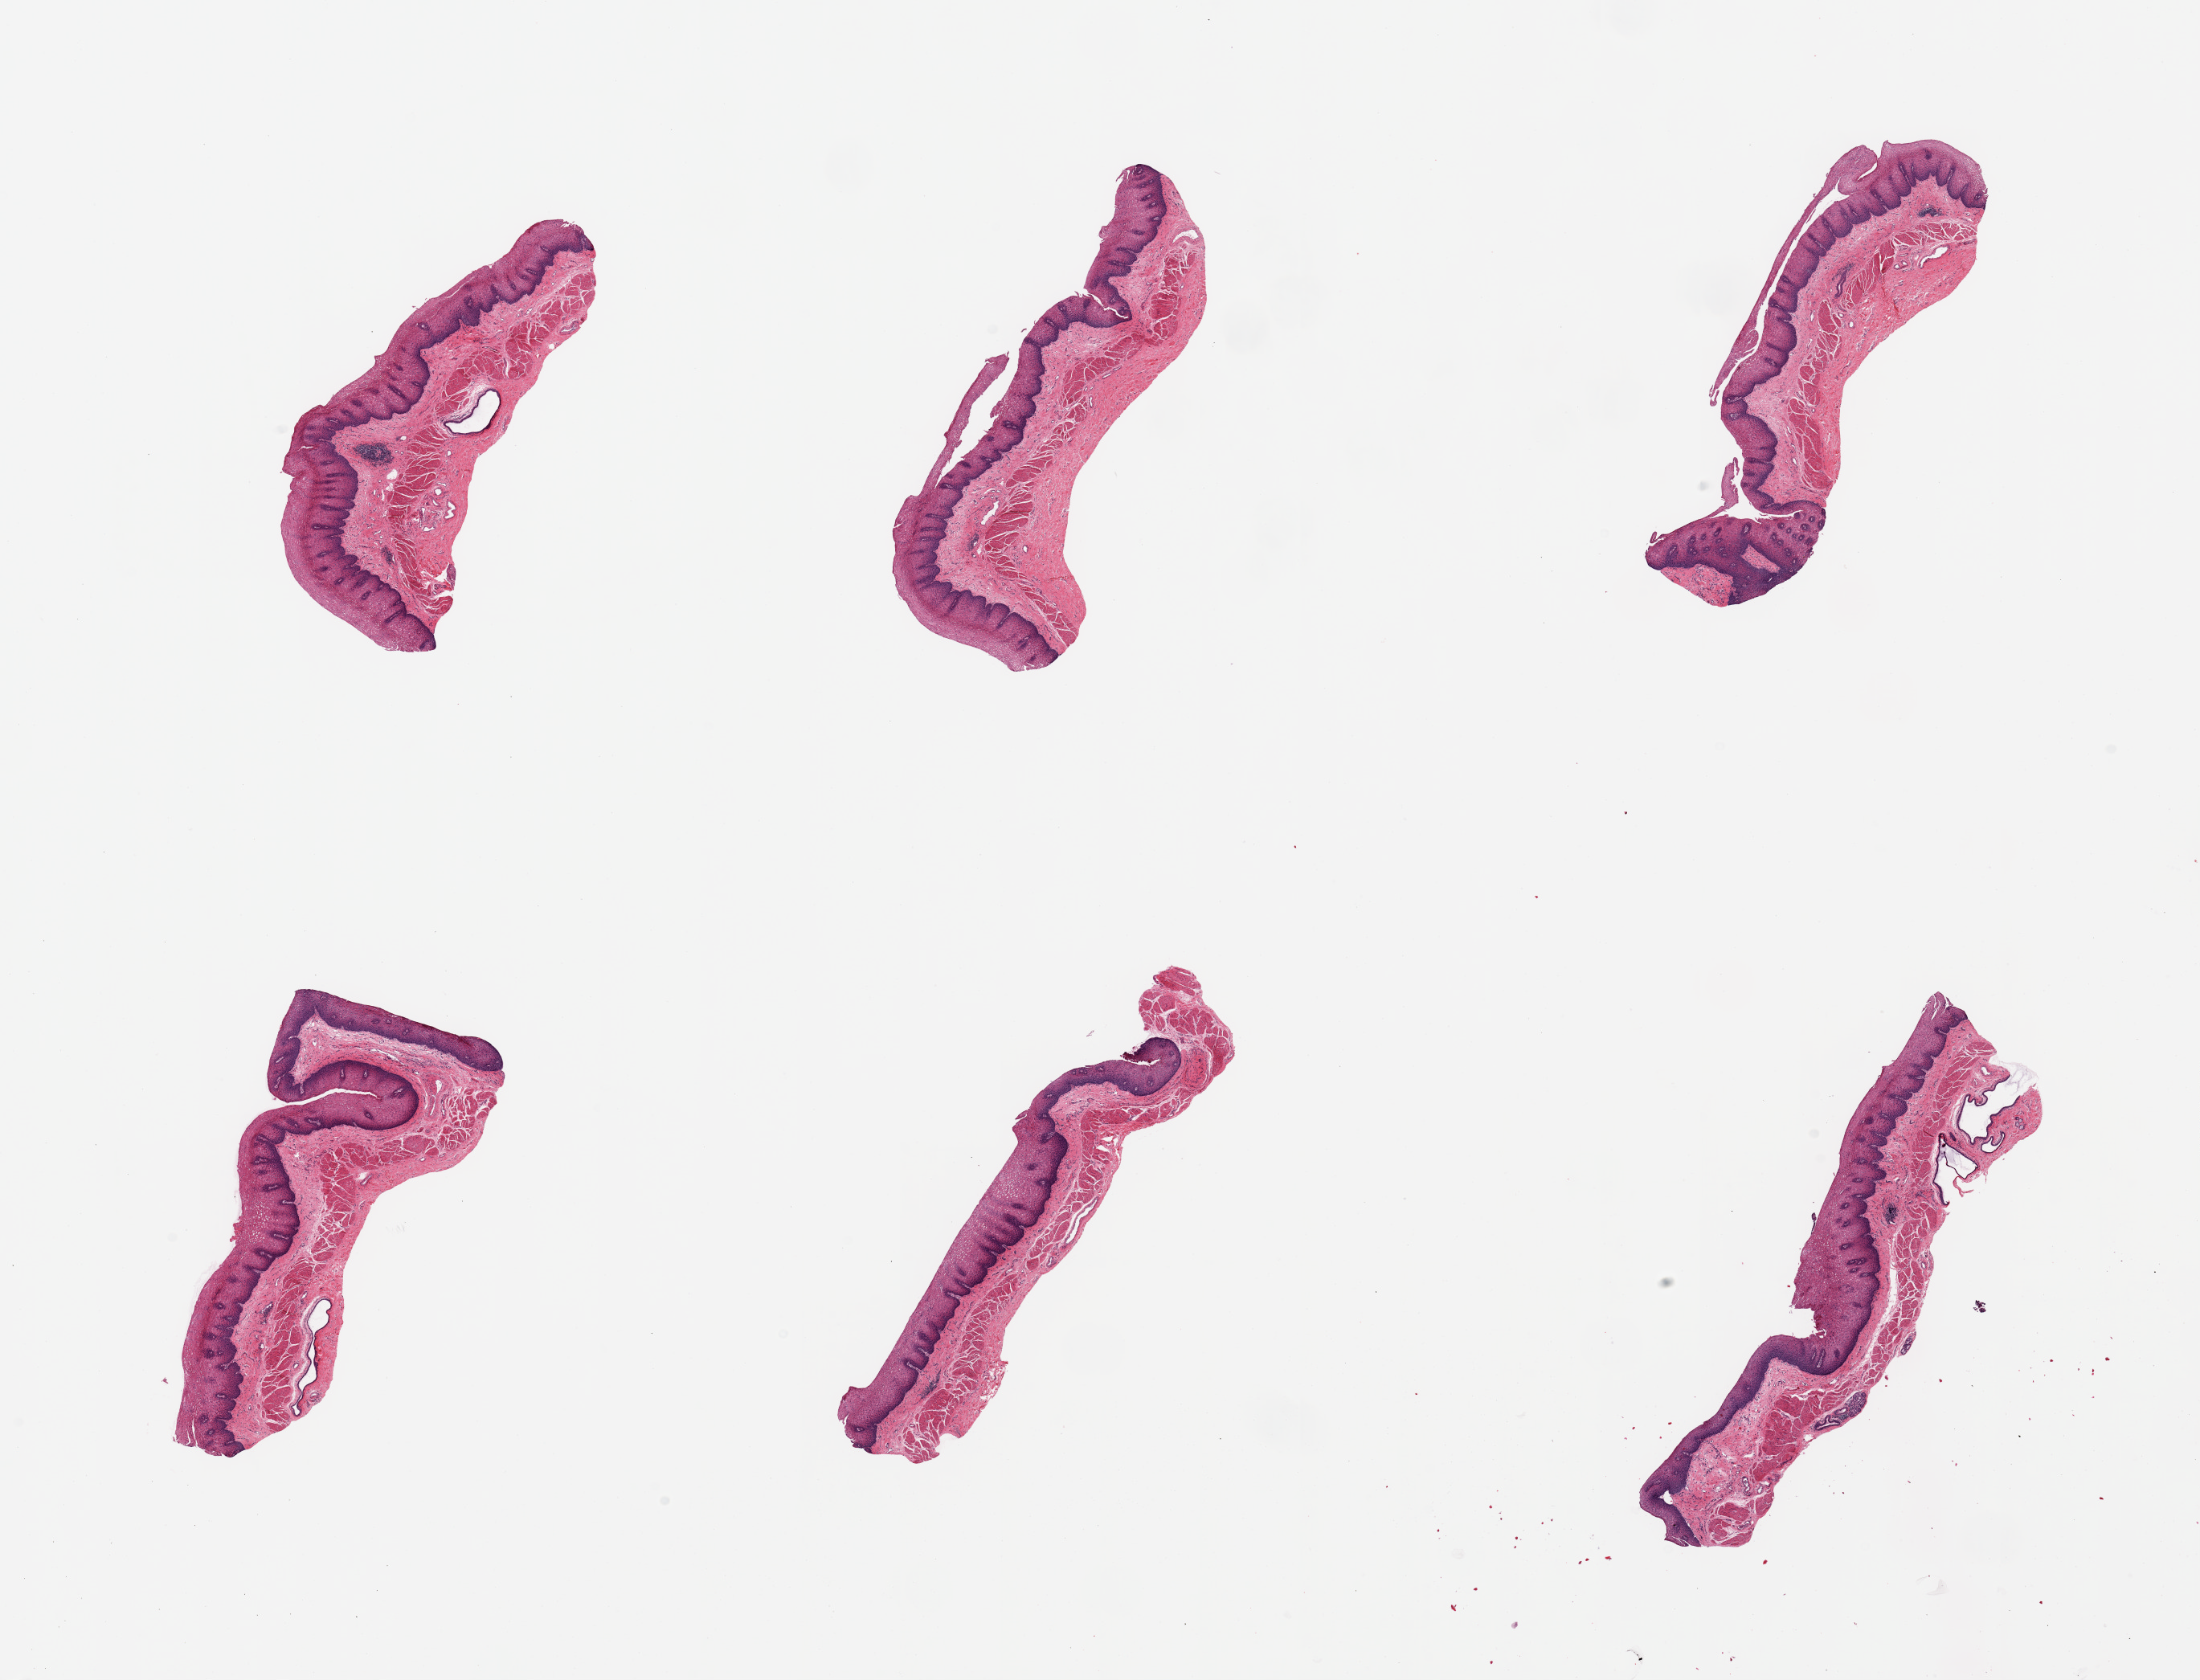
Whole-slide image, hematoxylin and eosin (H&E) stain, brightfield, shown as a low-resolution overview of the whole scanned area (about 21.7 x 16.5 mm). PAXgene-fixed paraffin-embedded (PFPE) section. Target tissue: esophageal mucous membrane. Donor tissue sample. Male donor.
Review note (as recorded): 6 pieces, squamous mucosa is ~0.5mm, ~20-25% total thickness.